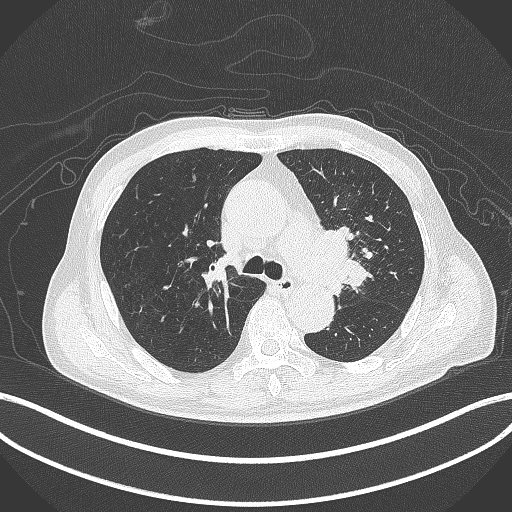
Chest CT, one axial slice. Position 286 of 417 along the scan axis. Reconstruction kernel B70f. Lung window (W 1500 / L -600 HU). 512 × 512 image matrix, field of view 400 × 400 mm. Male patient, age 77 years. Case-level facts recorded for this patient, not image findings: clinical TNM (as recorded): T3 N1 M0.
Outlined on this slice (rectangle marked by the reading radiologist):
- lung tumour (recorded histology: adenocarcinoma): bounding box <312,227,369,295> (left, top, right, bottom; pixels)